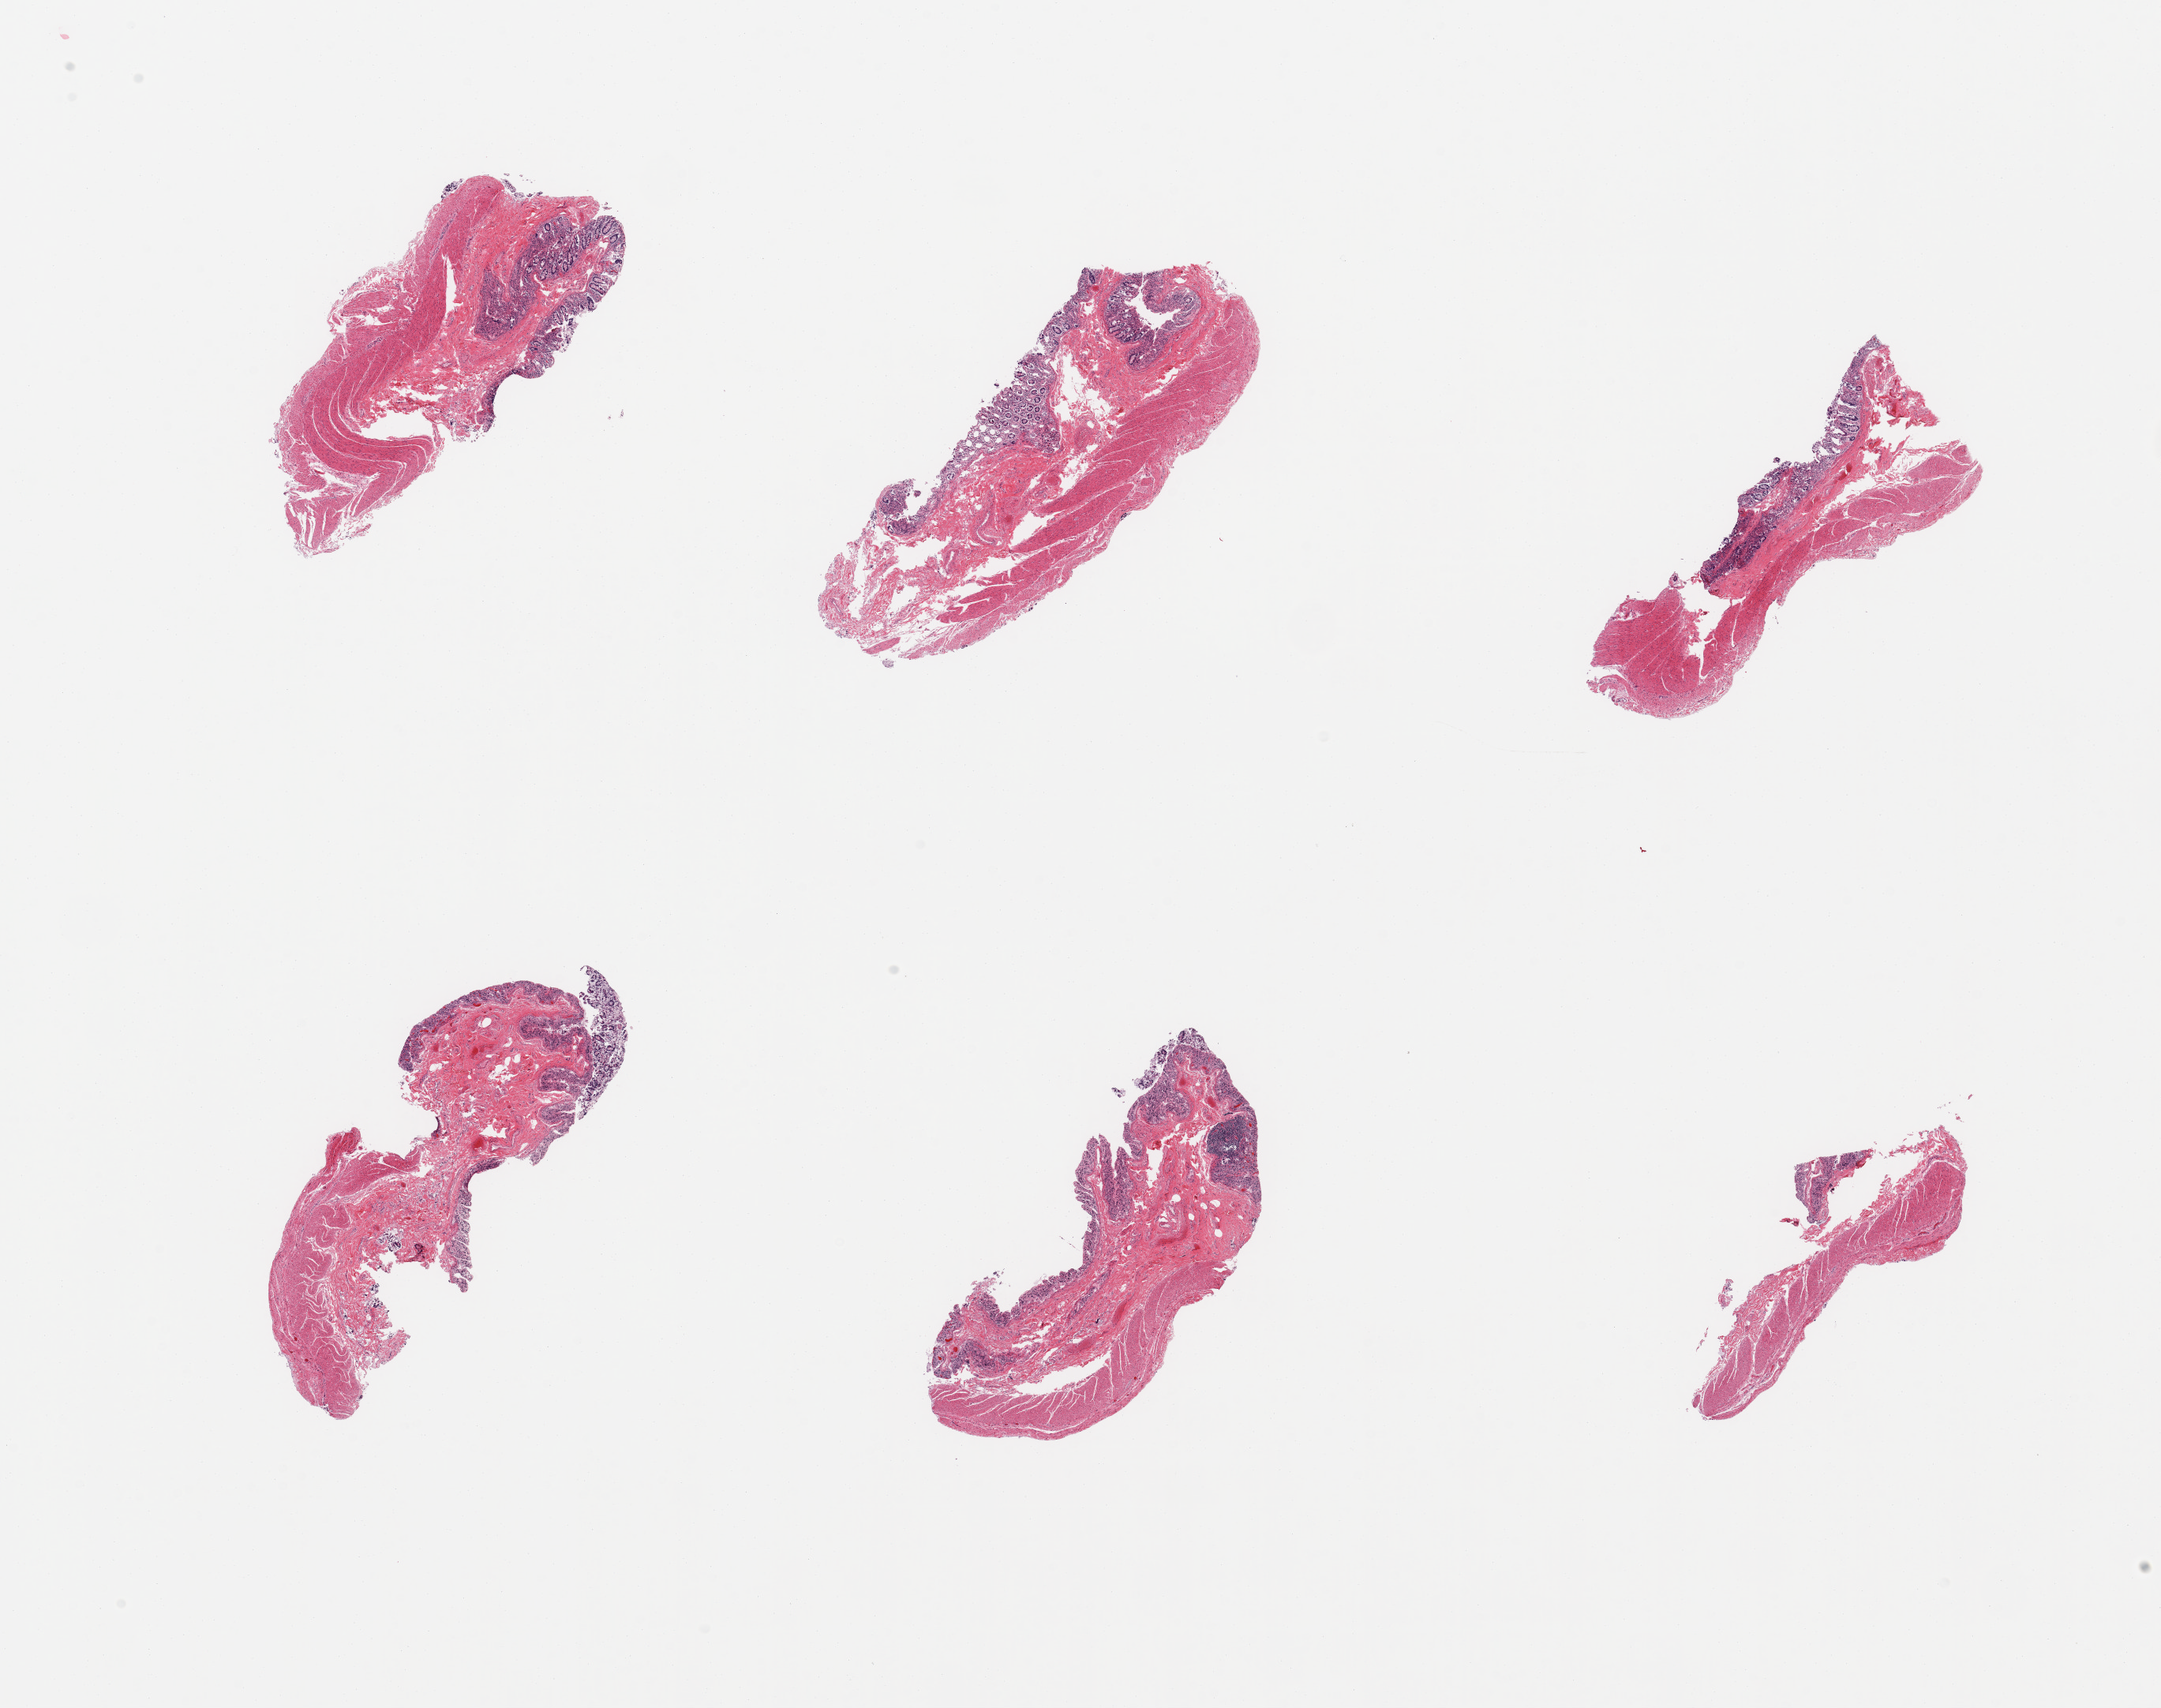
H&E whole-slide image, a low-resolution overview of the entire scanned area, about 21.7 x 17.1 mm. PAXgene-fixed, paraffin-embedded tissue. Target tissue: transverse colon. Donor tissue sample.
- pathologist's review note for this sample: 6 pieces, target mucosa with moderate-marked glandular autolysis